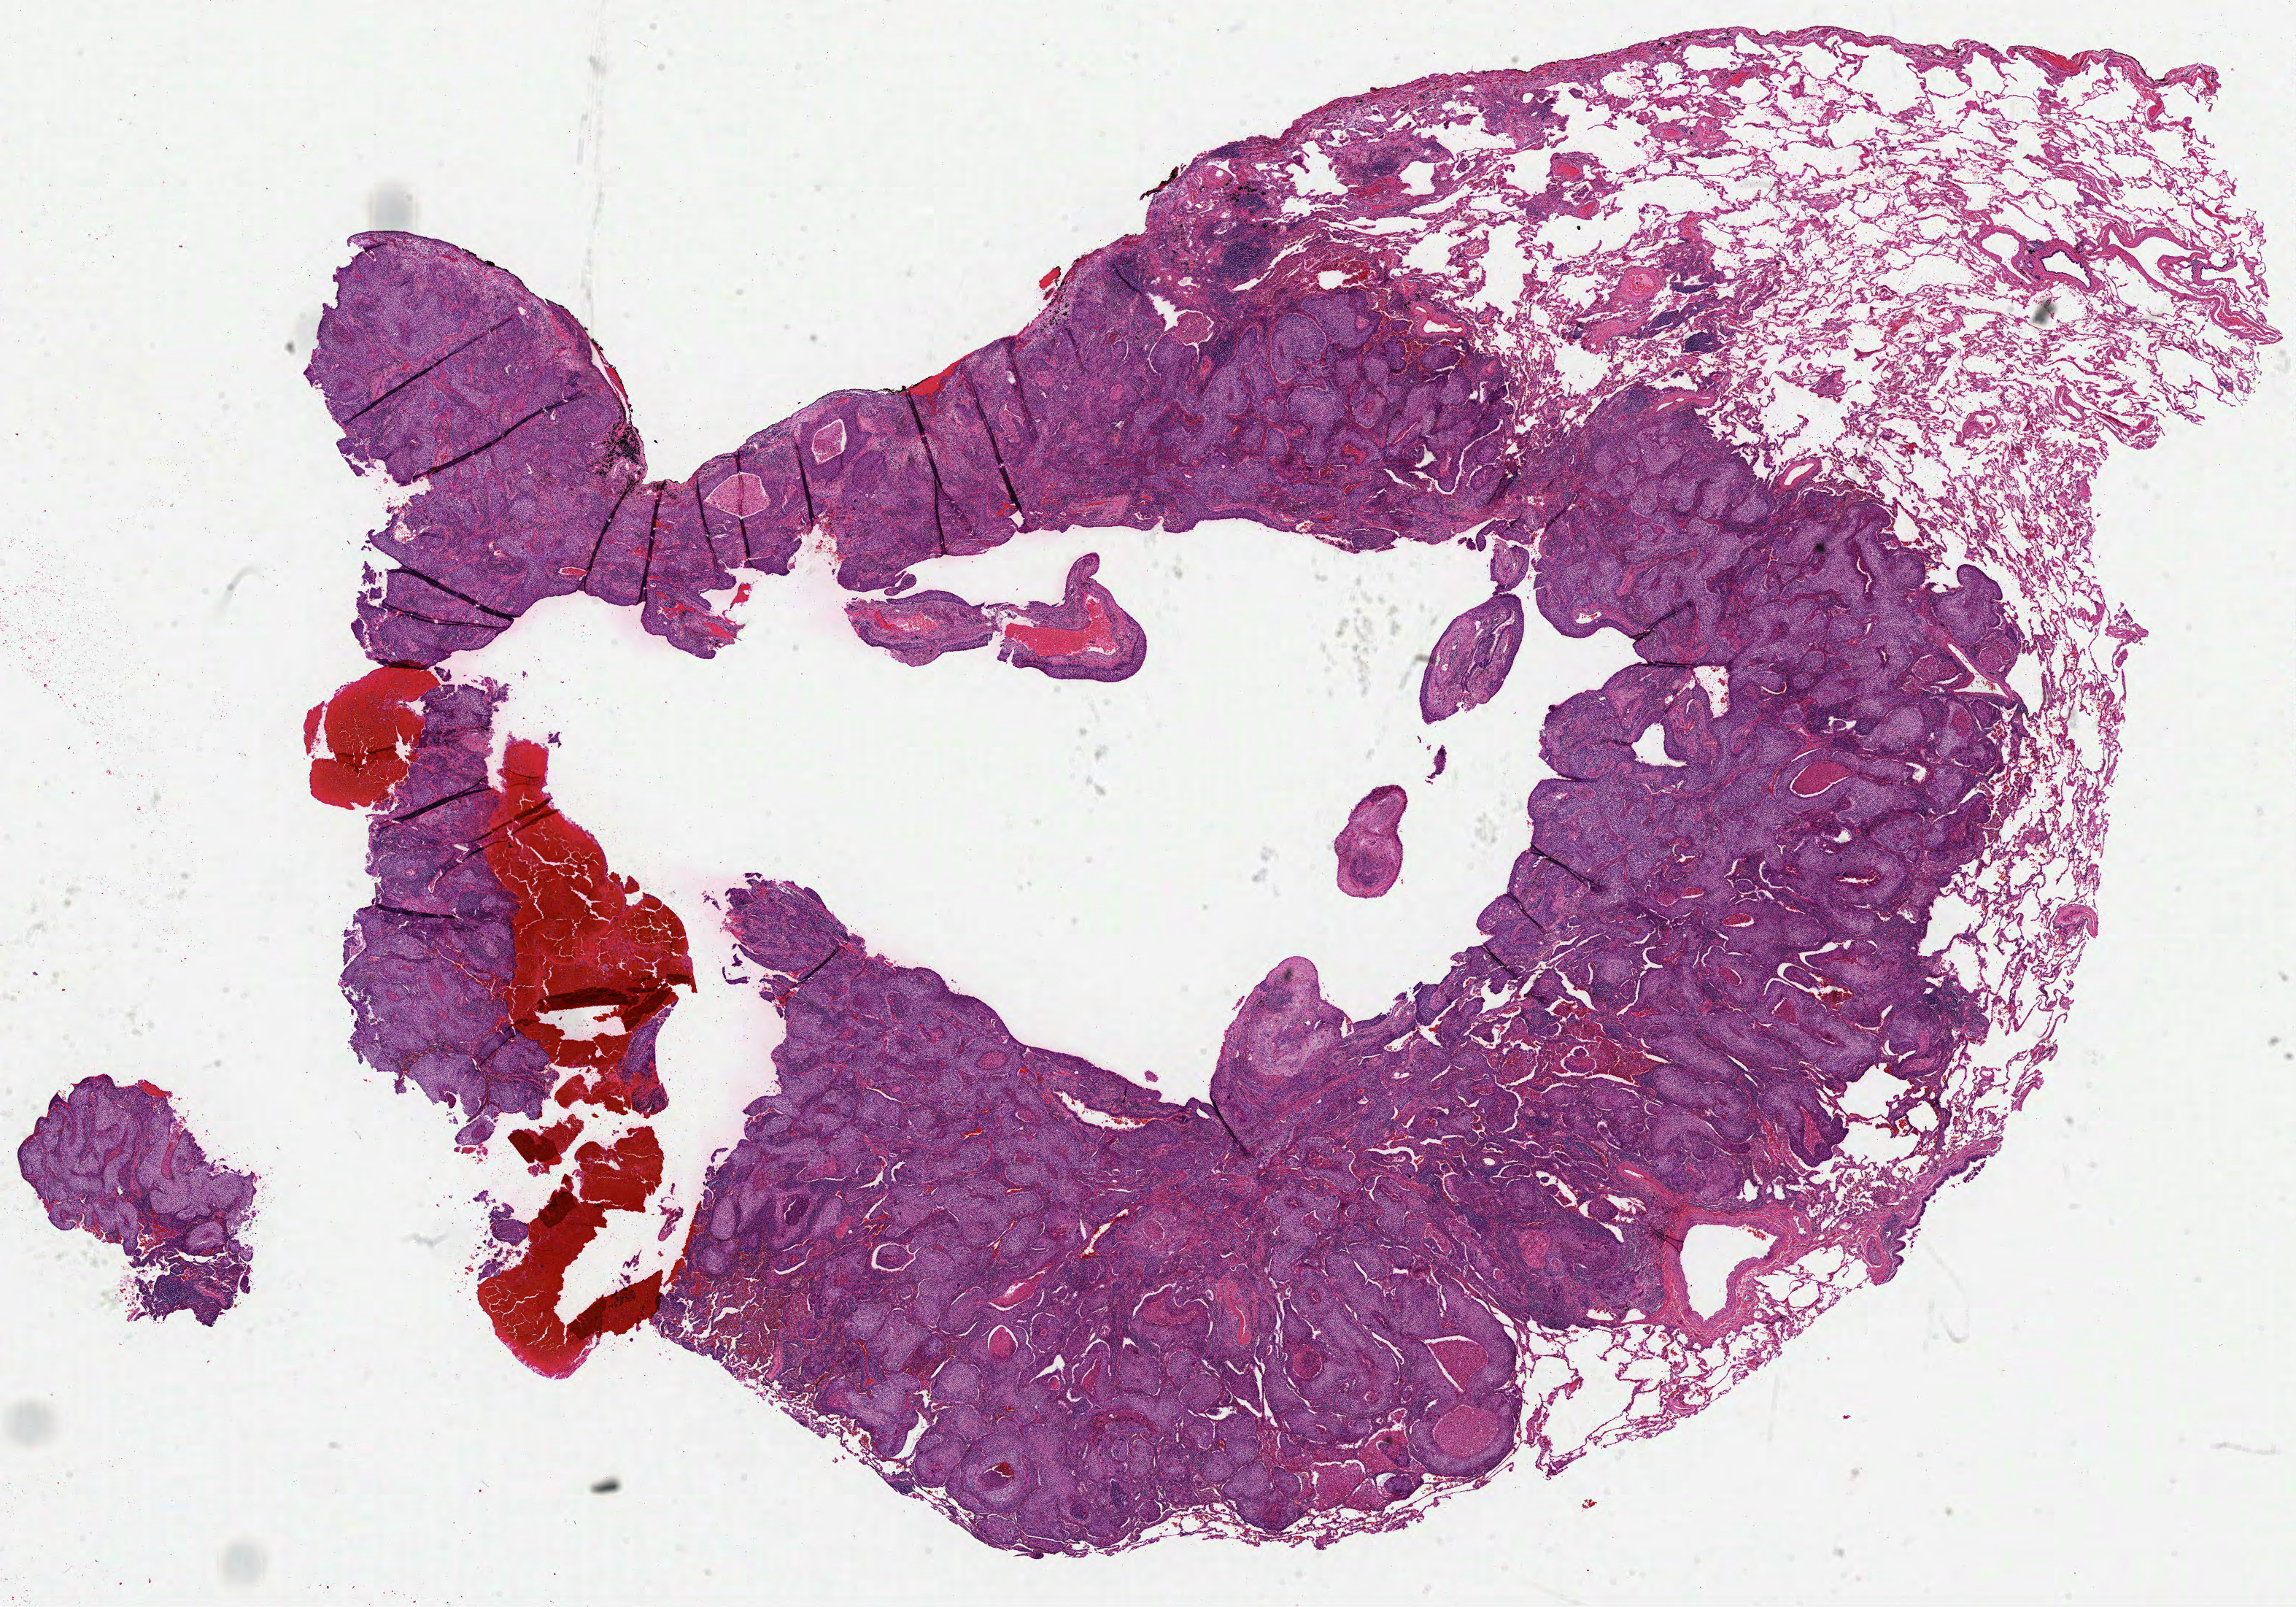
H&E-stained whole-slide image — shown as a low-resolution overview of the whole scanned area (about 25.4 x 17.8 mm, from a 40x scan). FFPE section. Lung, primary tumour sample. Patient: female, age at initial diagnosis 76 years.
AJCC pathologic stage: IB (5th edition). Laterality: left. Pathologic diagnosis: Squamous cell carcinoma, NOS.